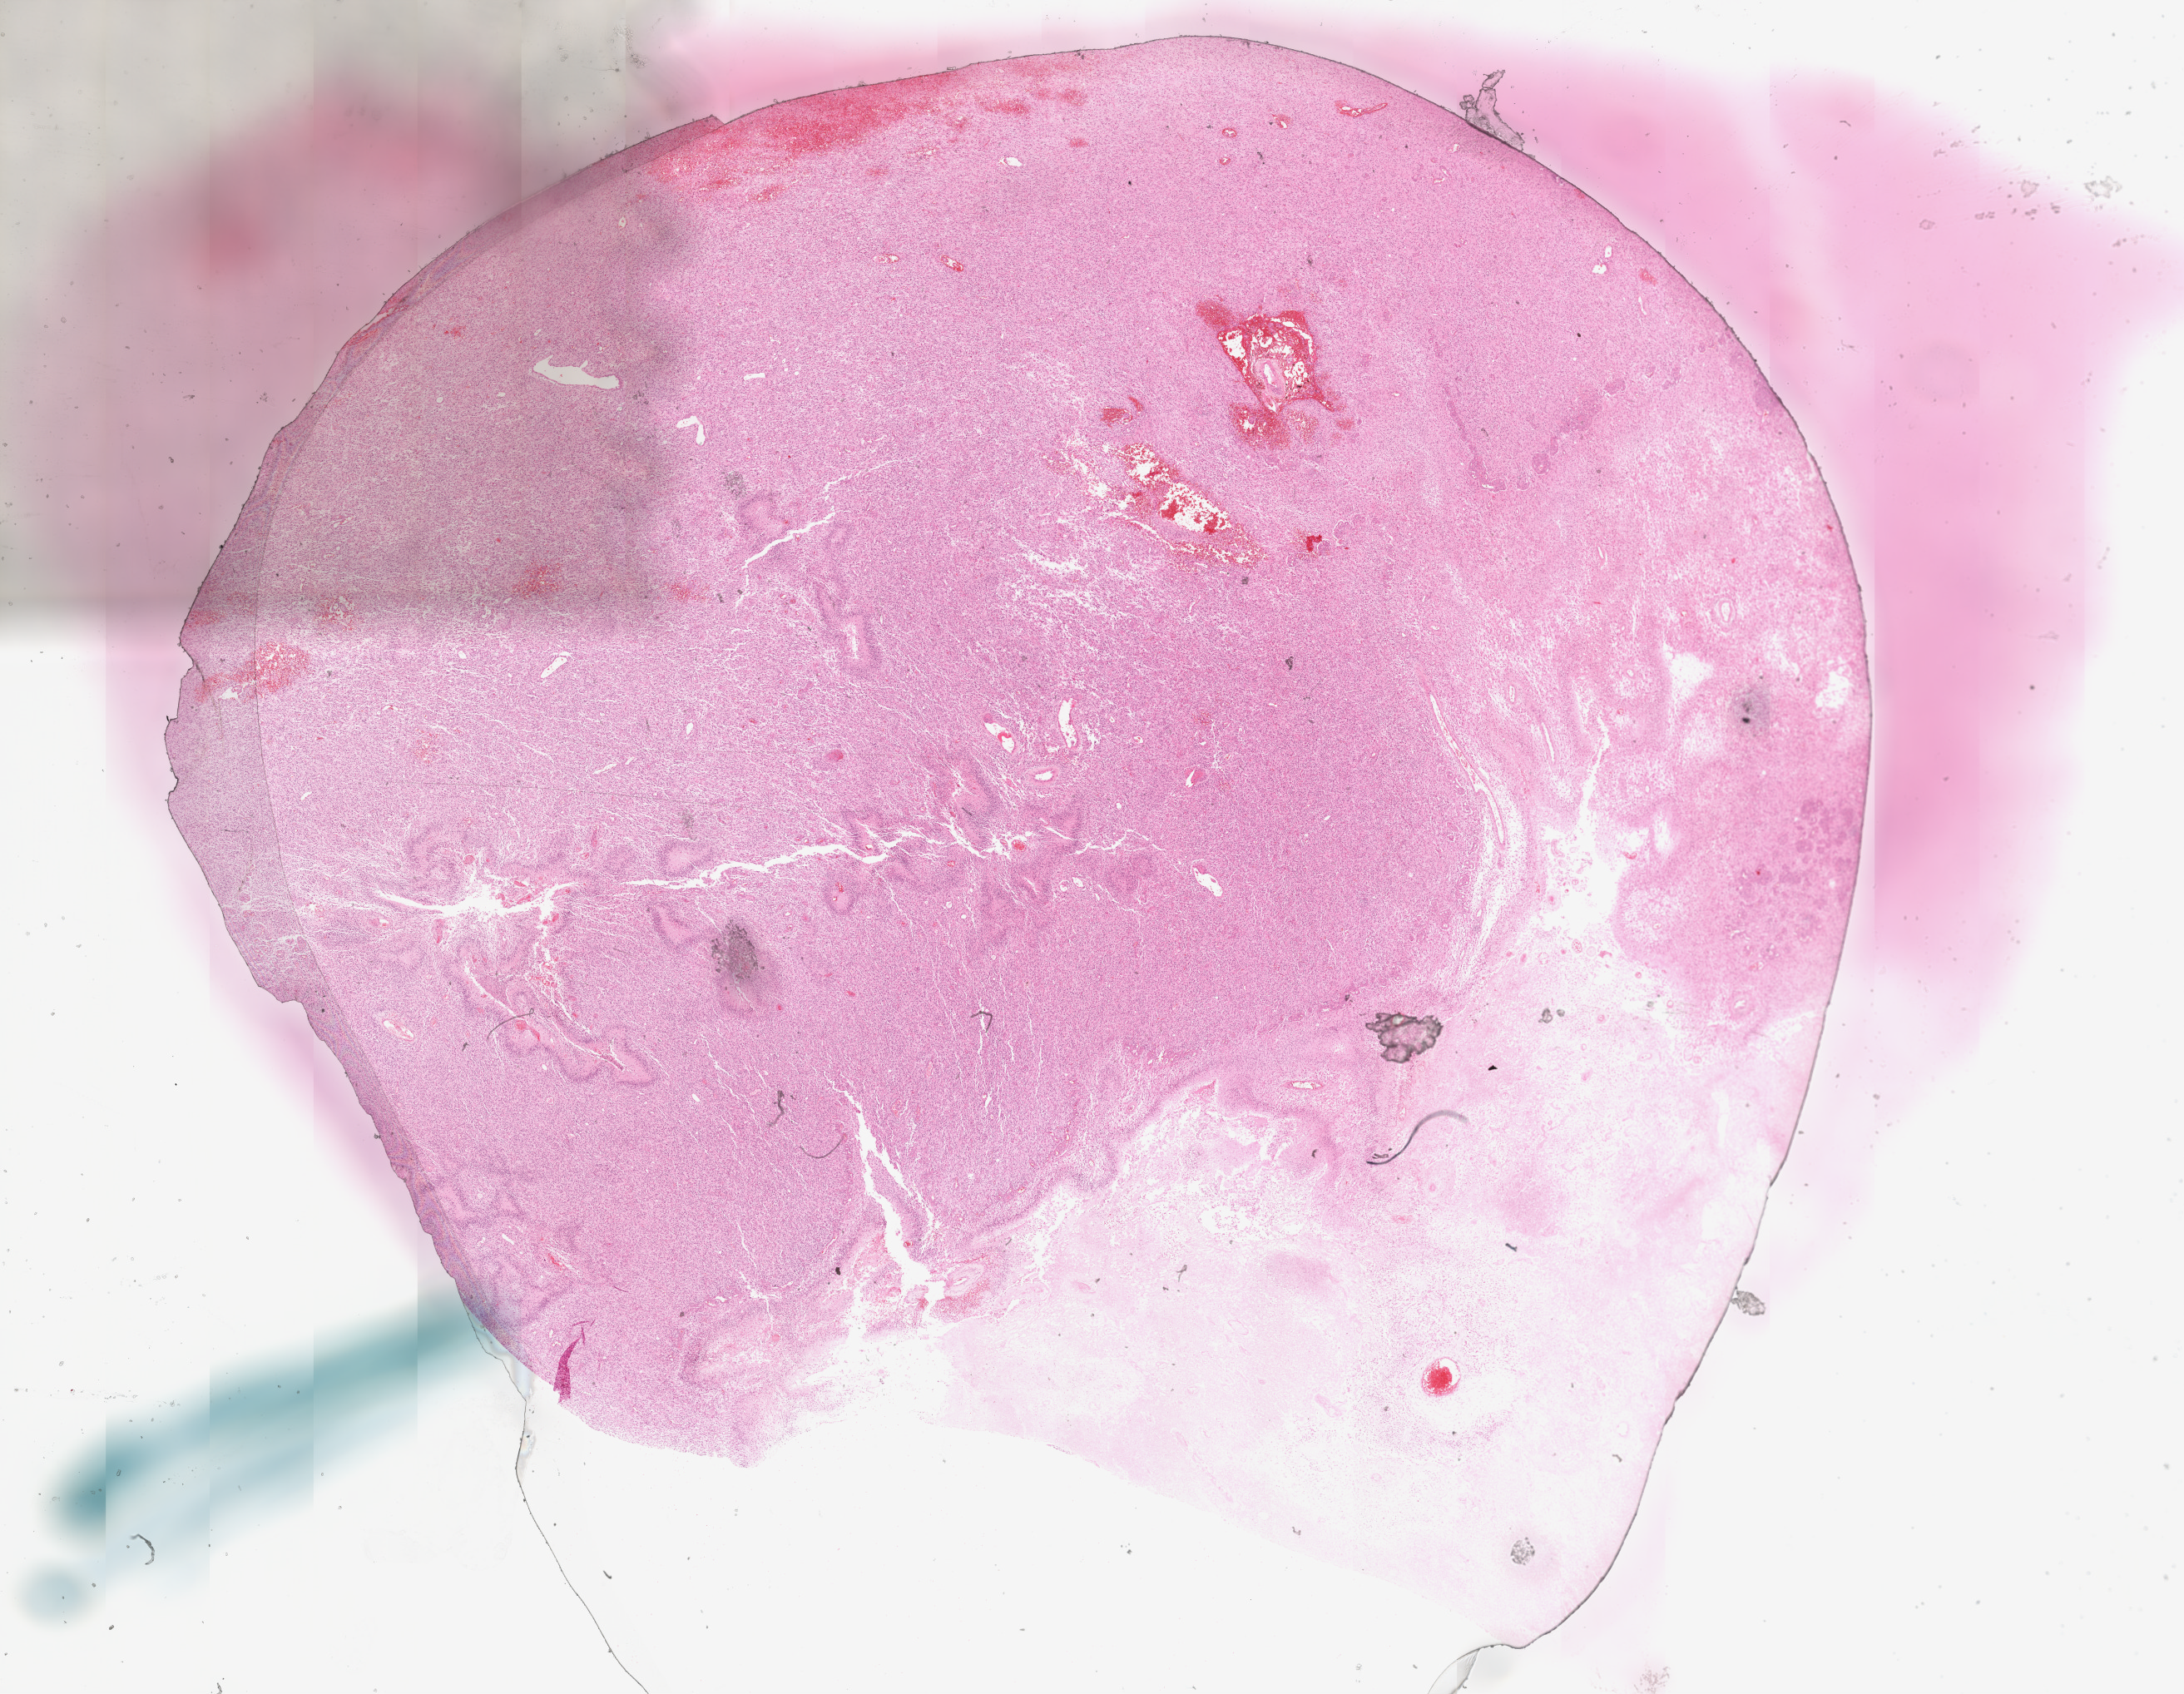
Whole-slide histology image, H&E — whole scanned area (about 21.1 x 16.3 mm, slide scanned at 20x) shown as a low-resolution overview, formalin-fixed paraffin-embedded (FFPE) diagnostic section, primary tumour sample from the brain. Male patient; age at initial diagnosis 50 years.
Diagnosis: Glioblastoma.